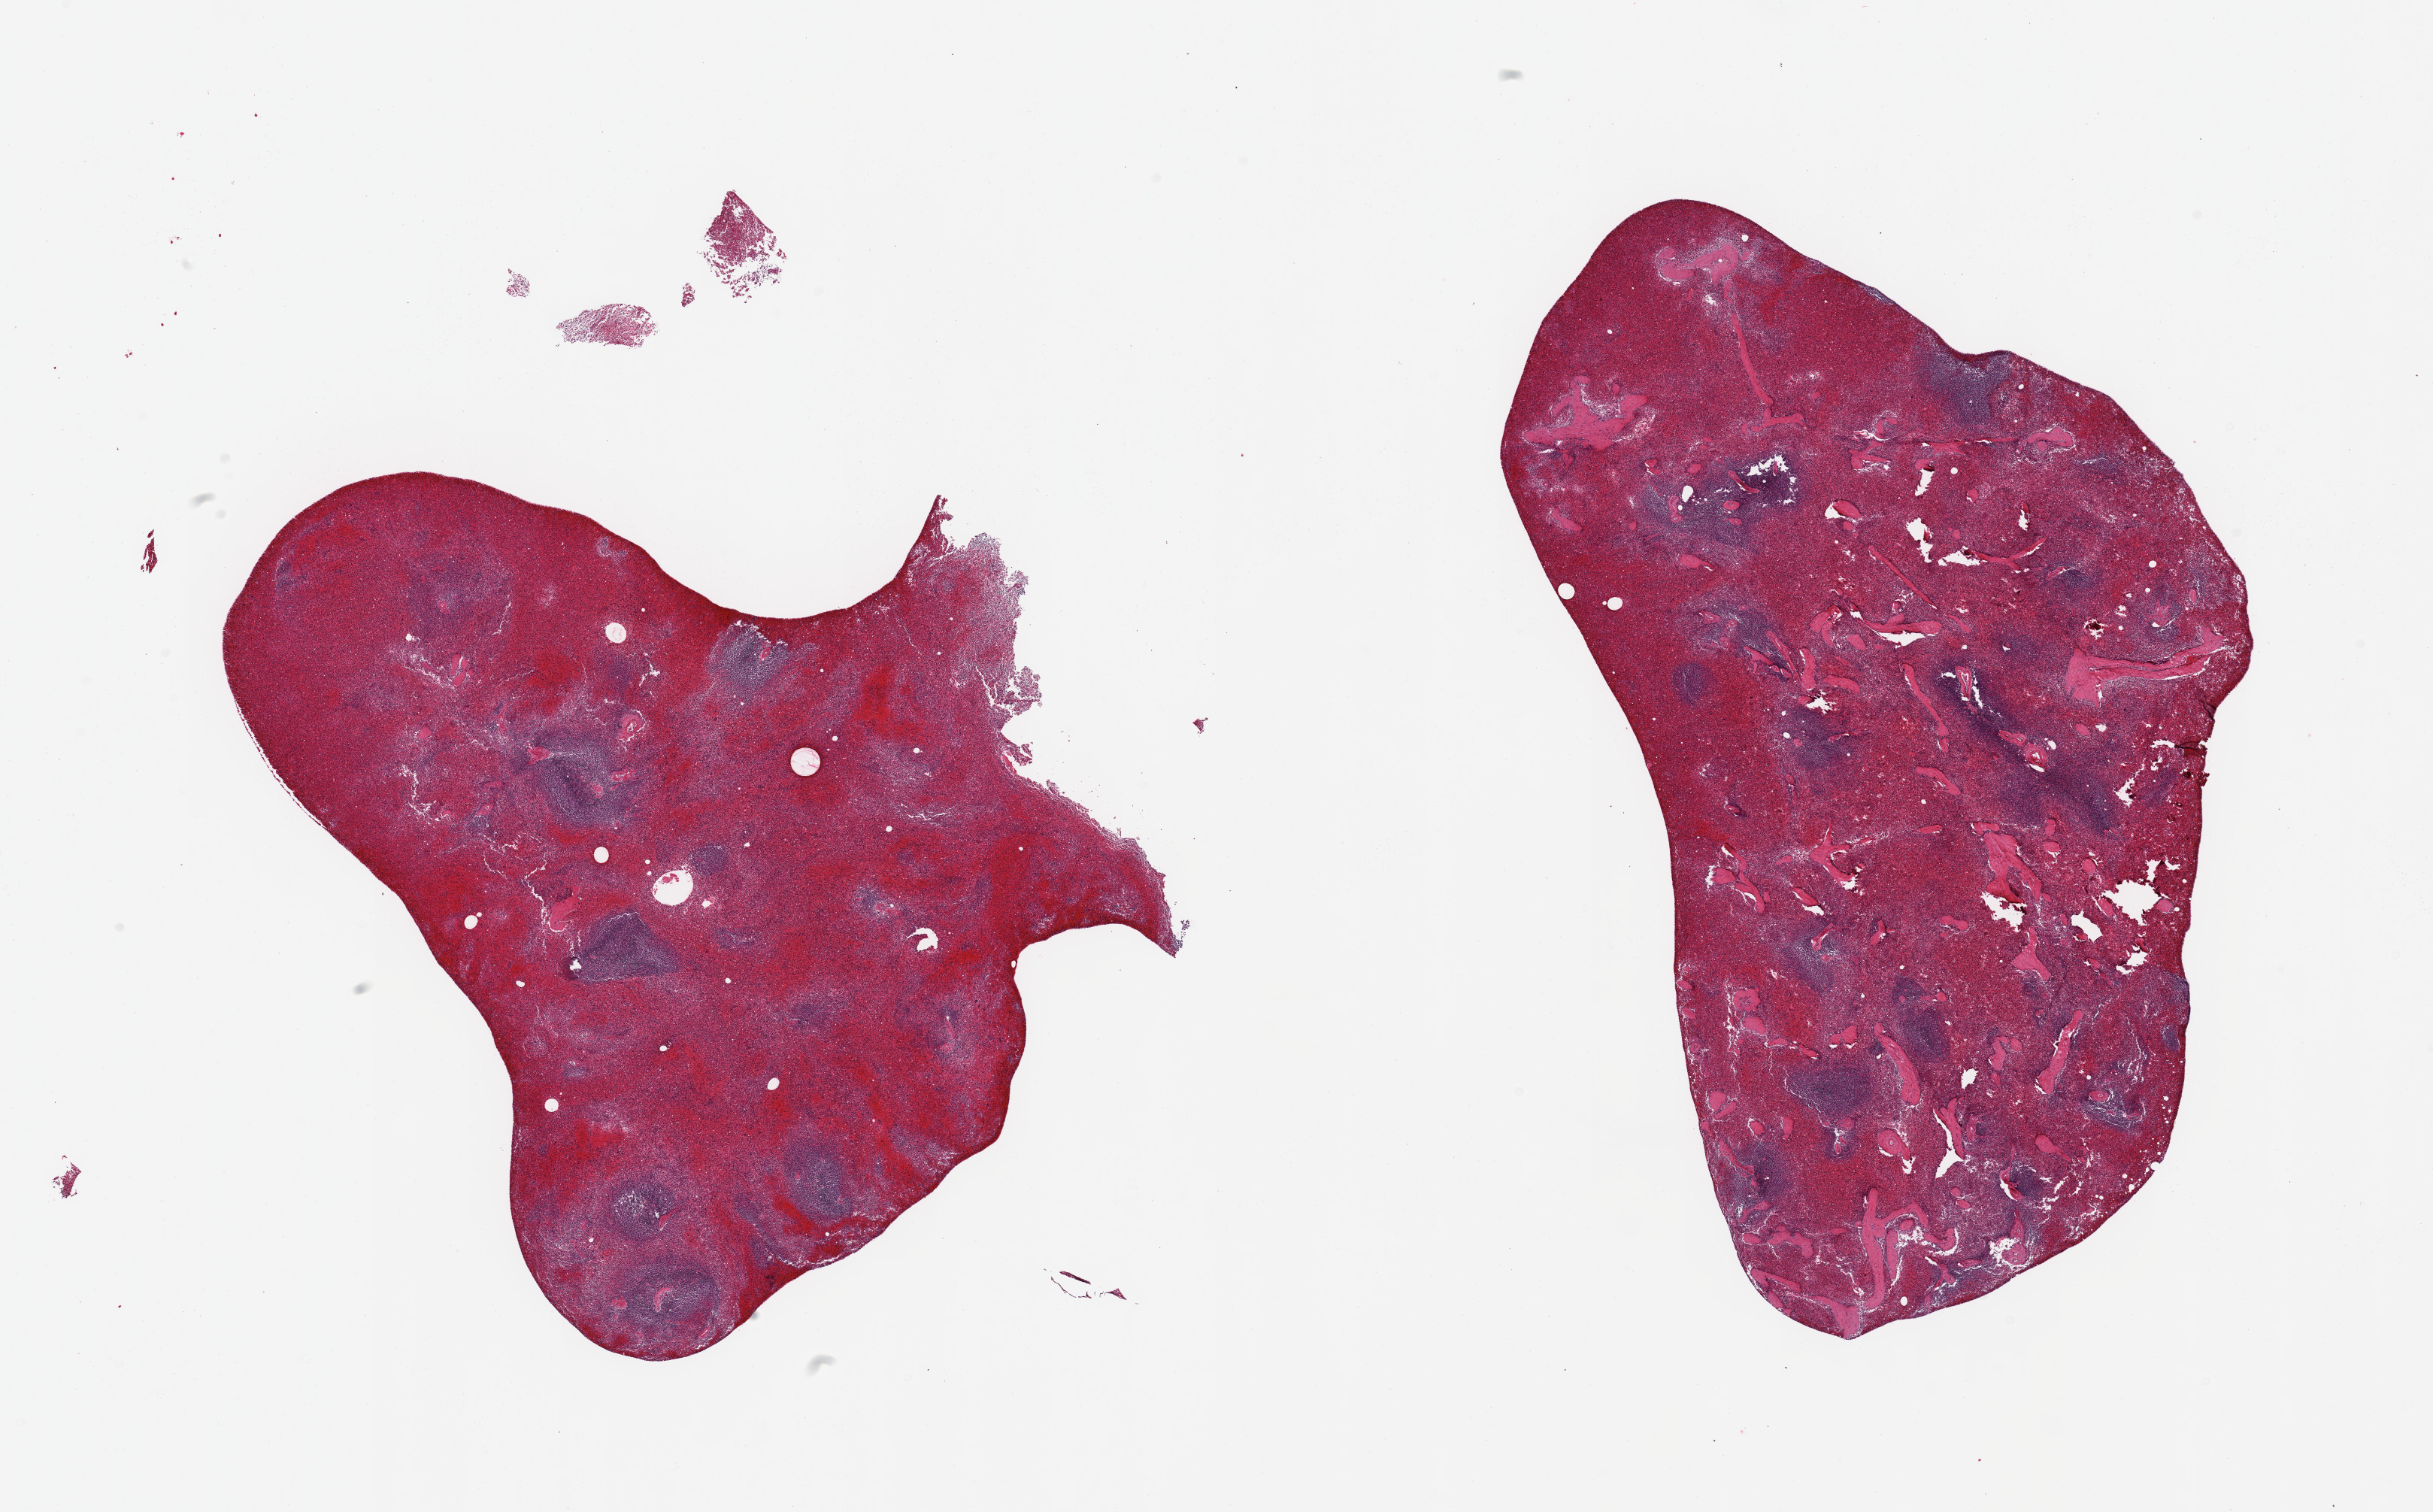
Digitized haematoxylin and eosin-stained section — low-resolution overview of the scanned area, about 25.6 x 15.9 mm (acquisition: 20x scan), PAXgene-fixed, paraffin-embedded tissue, section of spleen (target tissue), tissue donor sample. Donor sex: female.
Pathologist's review note for this sample: 2 pieces, moderate congestion.